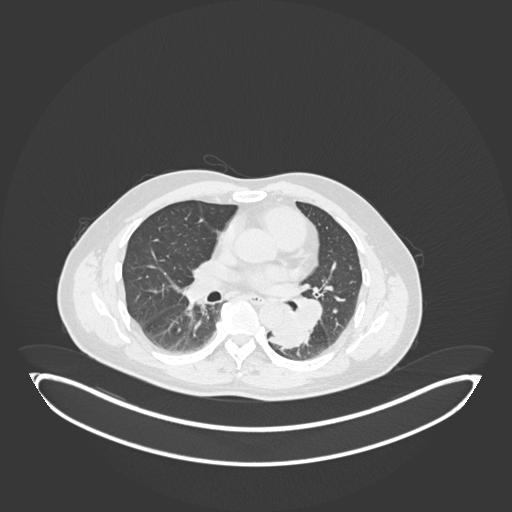
Chest CT, one axial slice. Position 104 of 258 along the scan axis. Reconstruction kernel B30f. 120 kVp. Lung window (W 1500 / L -600 HU). 512 × 512 image matrix, field of view 500 × 500 mm. Male patient, age 54 years. Case-level facts recorded for this patient, not image findings: clinical TNM (as recorded): T3 N0 M0.
Structures marked on this image (rectangle marked by the reading radiologist):
- lung tumour (recorded histology: squamous cell carcinoma): bounding box [x1, y1, x2, y2] px = [271, 314, 306, 352]